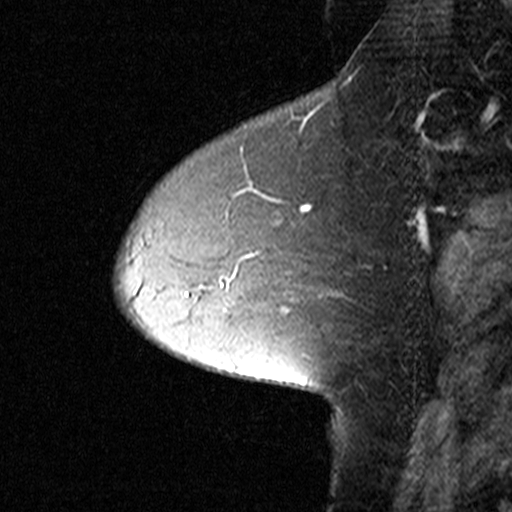
Breast MRI (dynamic contrast-enhanced), one sagittal slice. Position 13 of 44 along the scan axis. Dynamic contrast-enhanced study with each time point stored as its own series, time point 2 of 3 at this slice position (early post-contrast, ordered by acquisition time). 1.5 T. TE 4.5 ms, TR 11 ms. 512 × 512 image matrix, field of view 200 × 200 mm. Female patient, age 50 years. Case-level facts recorded for this patient, not image findings: setting: breast cancer imaged before/during neoadjuvant chemotherapy; receptor status: HR-positive, HER2-negative.
Outlined on this slice (semi-automatically segmented with operator editing):
- analysis volume of interest (the breast-tissue region the enhancement analysis was run in; not a lesion): bounding box (x1, y1, x2, y2) in pixels: (126, 162, 290, 291)
- tumour enhancement mask (voxels above the 90 % enhancement threshold inside the analysis volume of interest): (245, 166, 283, 254)